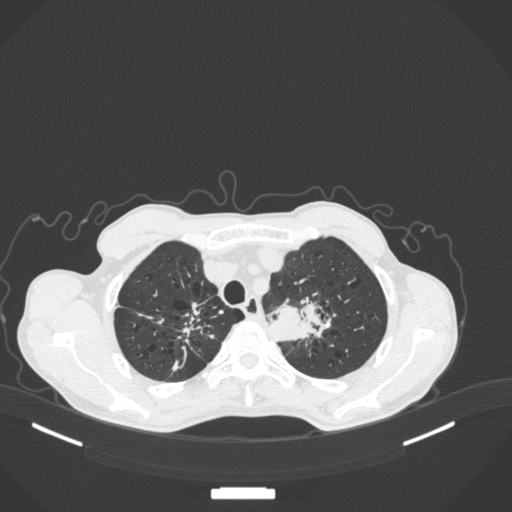
Chest CT, one axial slice. Slice 357 of 394 in the series (ordered by position). Lung window (W 1500 / L -600 HU). 1 mm slice thickness. 512 × 512 image matrix, field of view 400 × 400 mm. Patient: male, 65 years. Case-level facts recorded for this patient, not image findings: clinical TNM (as recorded): T2b N0 M0.
Annotated regions visible in this slice (rectangle marked by the reading radiologist):
- lung tumour (recorded histology: adenocarcinoma): bounding box [x1, y1, x2, y2] px = [260, 298, 337, 343]